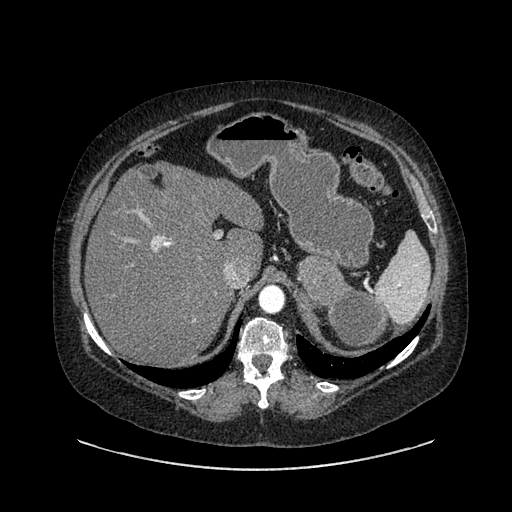
Contrast-enhanced abdominal CT, one axial slice; position 619 of 769 along the scan axis; 120 kVp; soft-tissue window (W 400 / L 40 HU); 0.62 mm slice thickness; 512 × 512 image matrix, field of view 460 × 460 mm. Female patient, age 61 years. From the clinical record (not read from this slice): diagnosis: adrenocortical carcinoma; tumour side: left adrenal; tumour size at pathology: 13 cm; Ki-67 index: 79 %; stage (as recorded): 2.
Structures marked on this image (semi-automatic segmentation, software-assisted and operator-edited):
- mass: bounding box (x1, y1, x2, y2) in pixels: (298, 223, 512, 349)